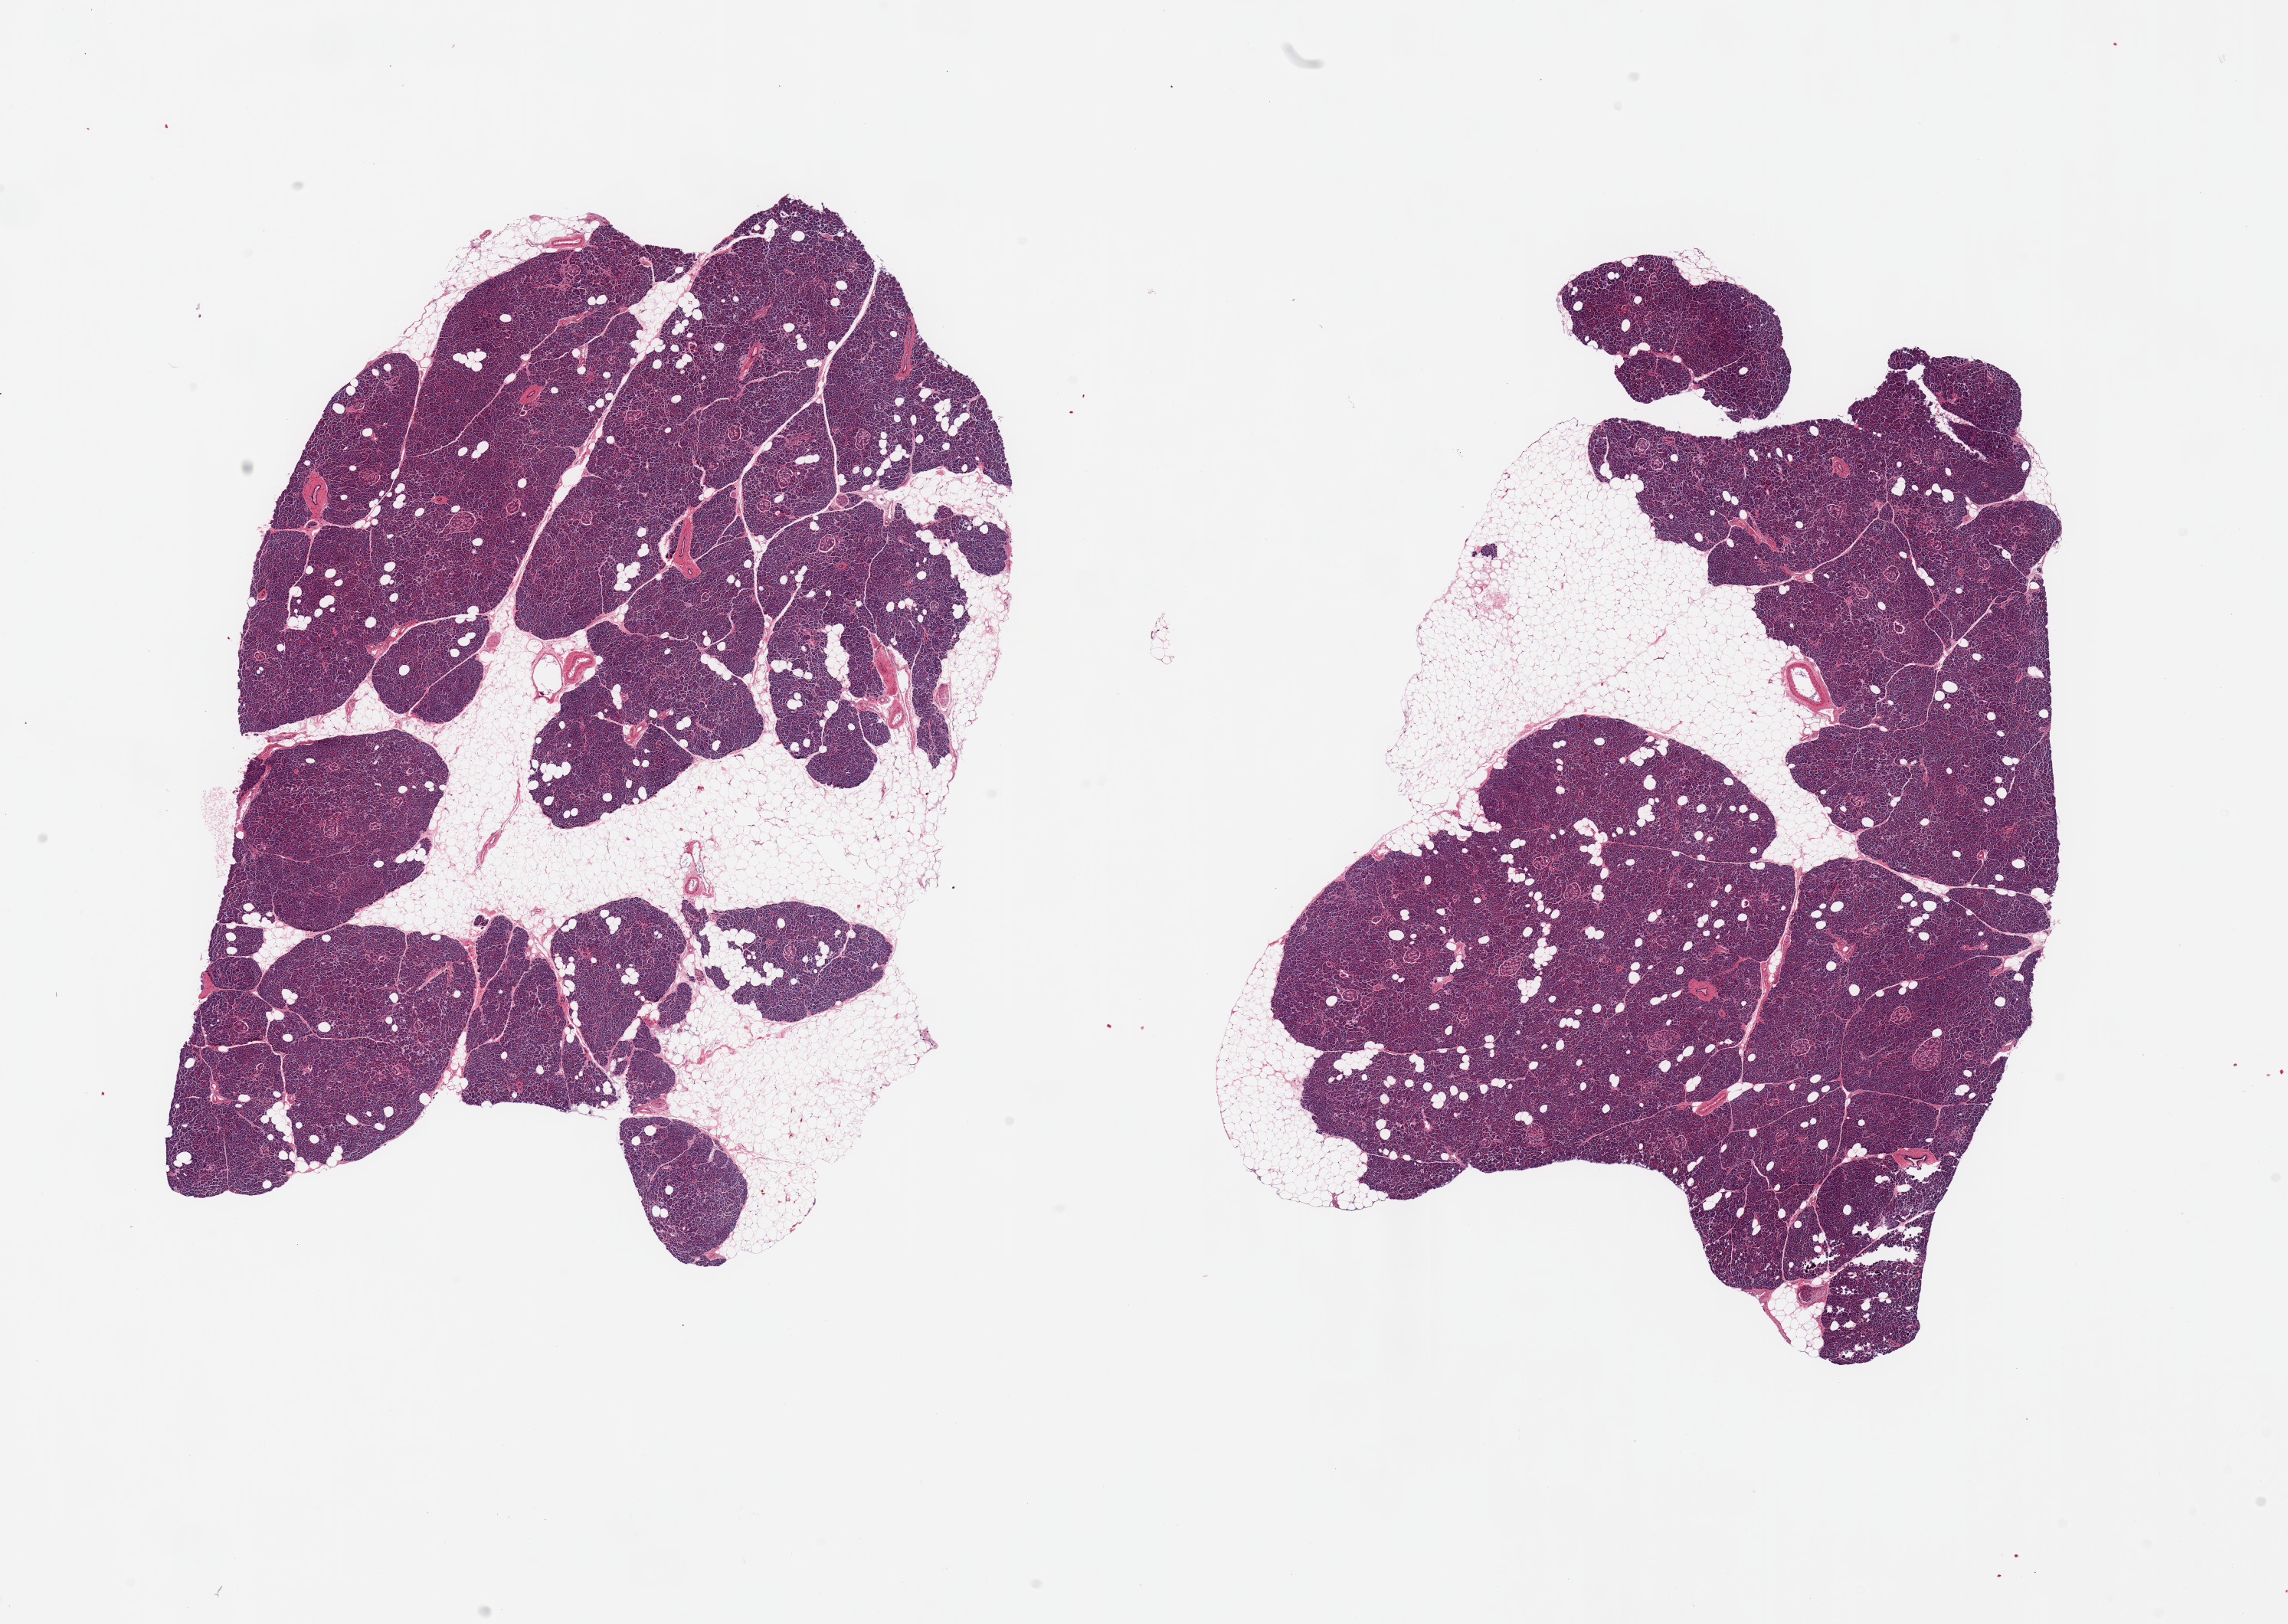
Digitized haematoxylin and eosin-stained section, brightfield — shown as a low-resolution overview of the whole scanned area (about 23.6 x 16.8 mm, from a 20x scan); PAXgene-fixed paraffin-embedded (PFPE) section; section of pancreas (target tissue); donor tissue sample.
Reviewer comment on this tissue sample: 2 pieces, moderate saponification; Islets beginning to degrade.